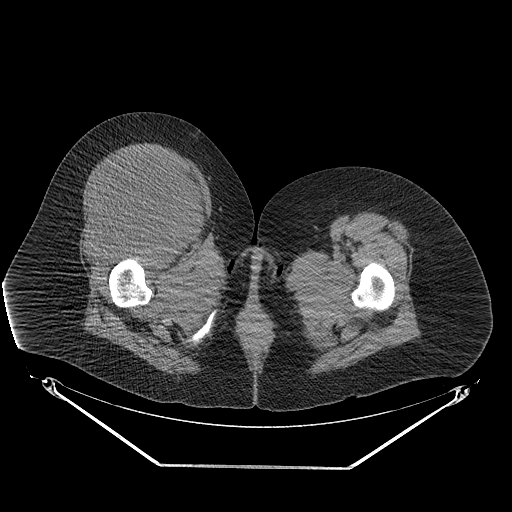
CT of an extremity soft-tissue mass (from a PET/CT study), one axial slice. Position 50 of 267 along the scan axis. 140 kVp. Soft-tissue window (W 400 / L 40 HU). 3.75 mm slice thickness. 512 × 512 image matrix, field of view 500 × 500 mm. Female patient. From the clinical record (not read from this slice): histological type: malignant solitary fibrous tumor; grade: intermediate; site of the primary tumour: right thigh.
Outlined on this slice (expert contour drawn on MRI and transferred to this co-registered scan by the dataset authors):
- gross tumour volume including surrounding oedema: bounding box [x1, y1, x2, y2] px = [75, 151, 204, 245]
- gross tumour volume (mass): [80, 151, 200, 243]